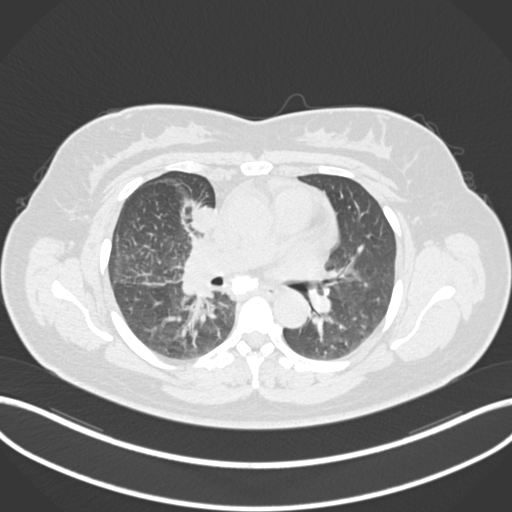
Chest CT, one axial slice. Reconstruction kernel B30f. Lung window (W 1500 / L -600 HU). 1 mm slice thickness. 512 × 512 image matrix. Patient: female, 46 years. Case-level facts recorded for this patient, not image findings: clinical TNM (as recorded): T2a N1 M0.
Outlined on this slice (bounding box drawn by a radiologist):
- lung tumour (recorded histology: adenocarcinoma): box from (x=187, y=200) to (x=224, y=240) px